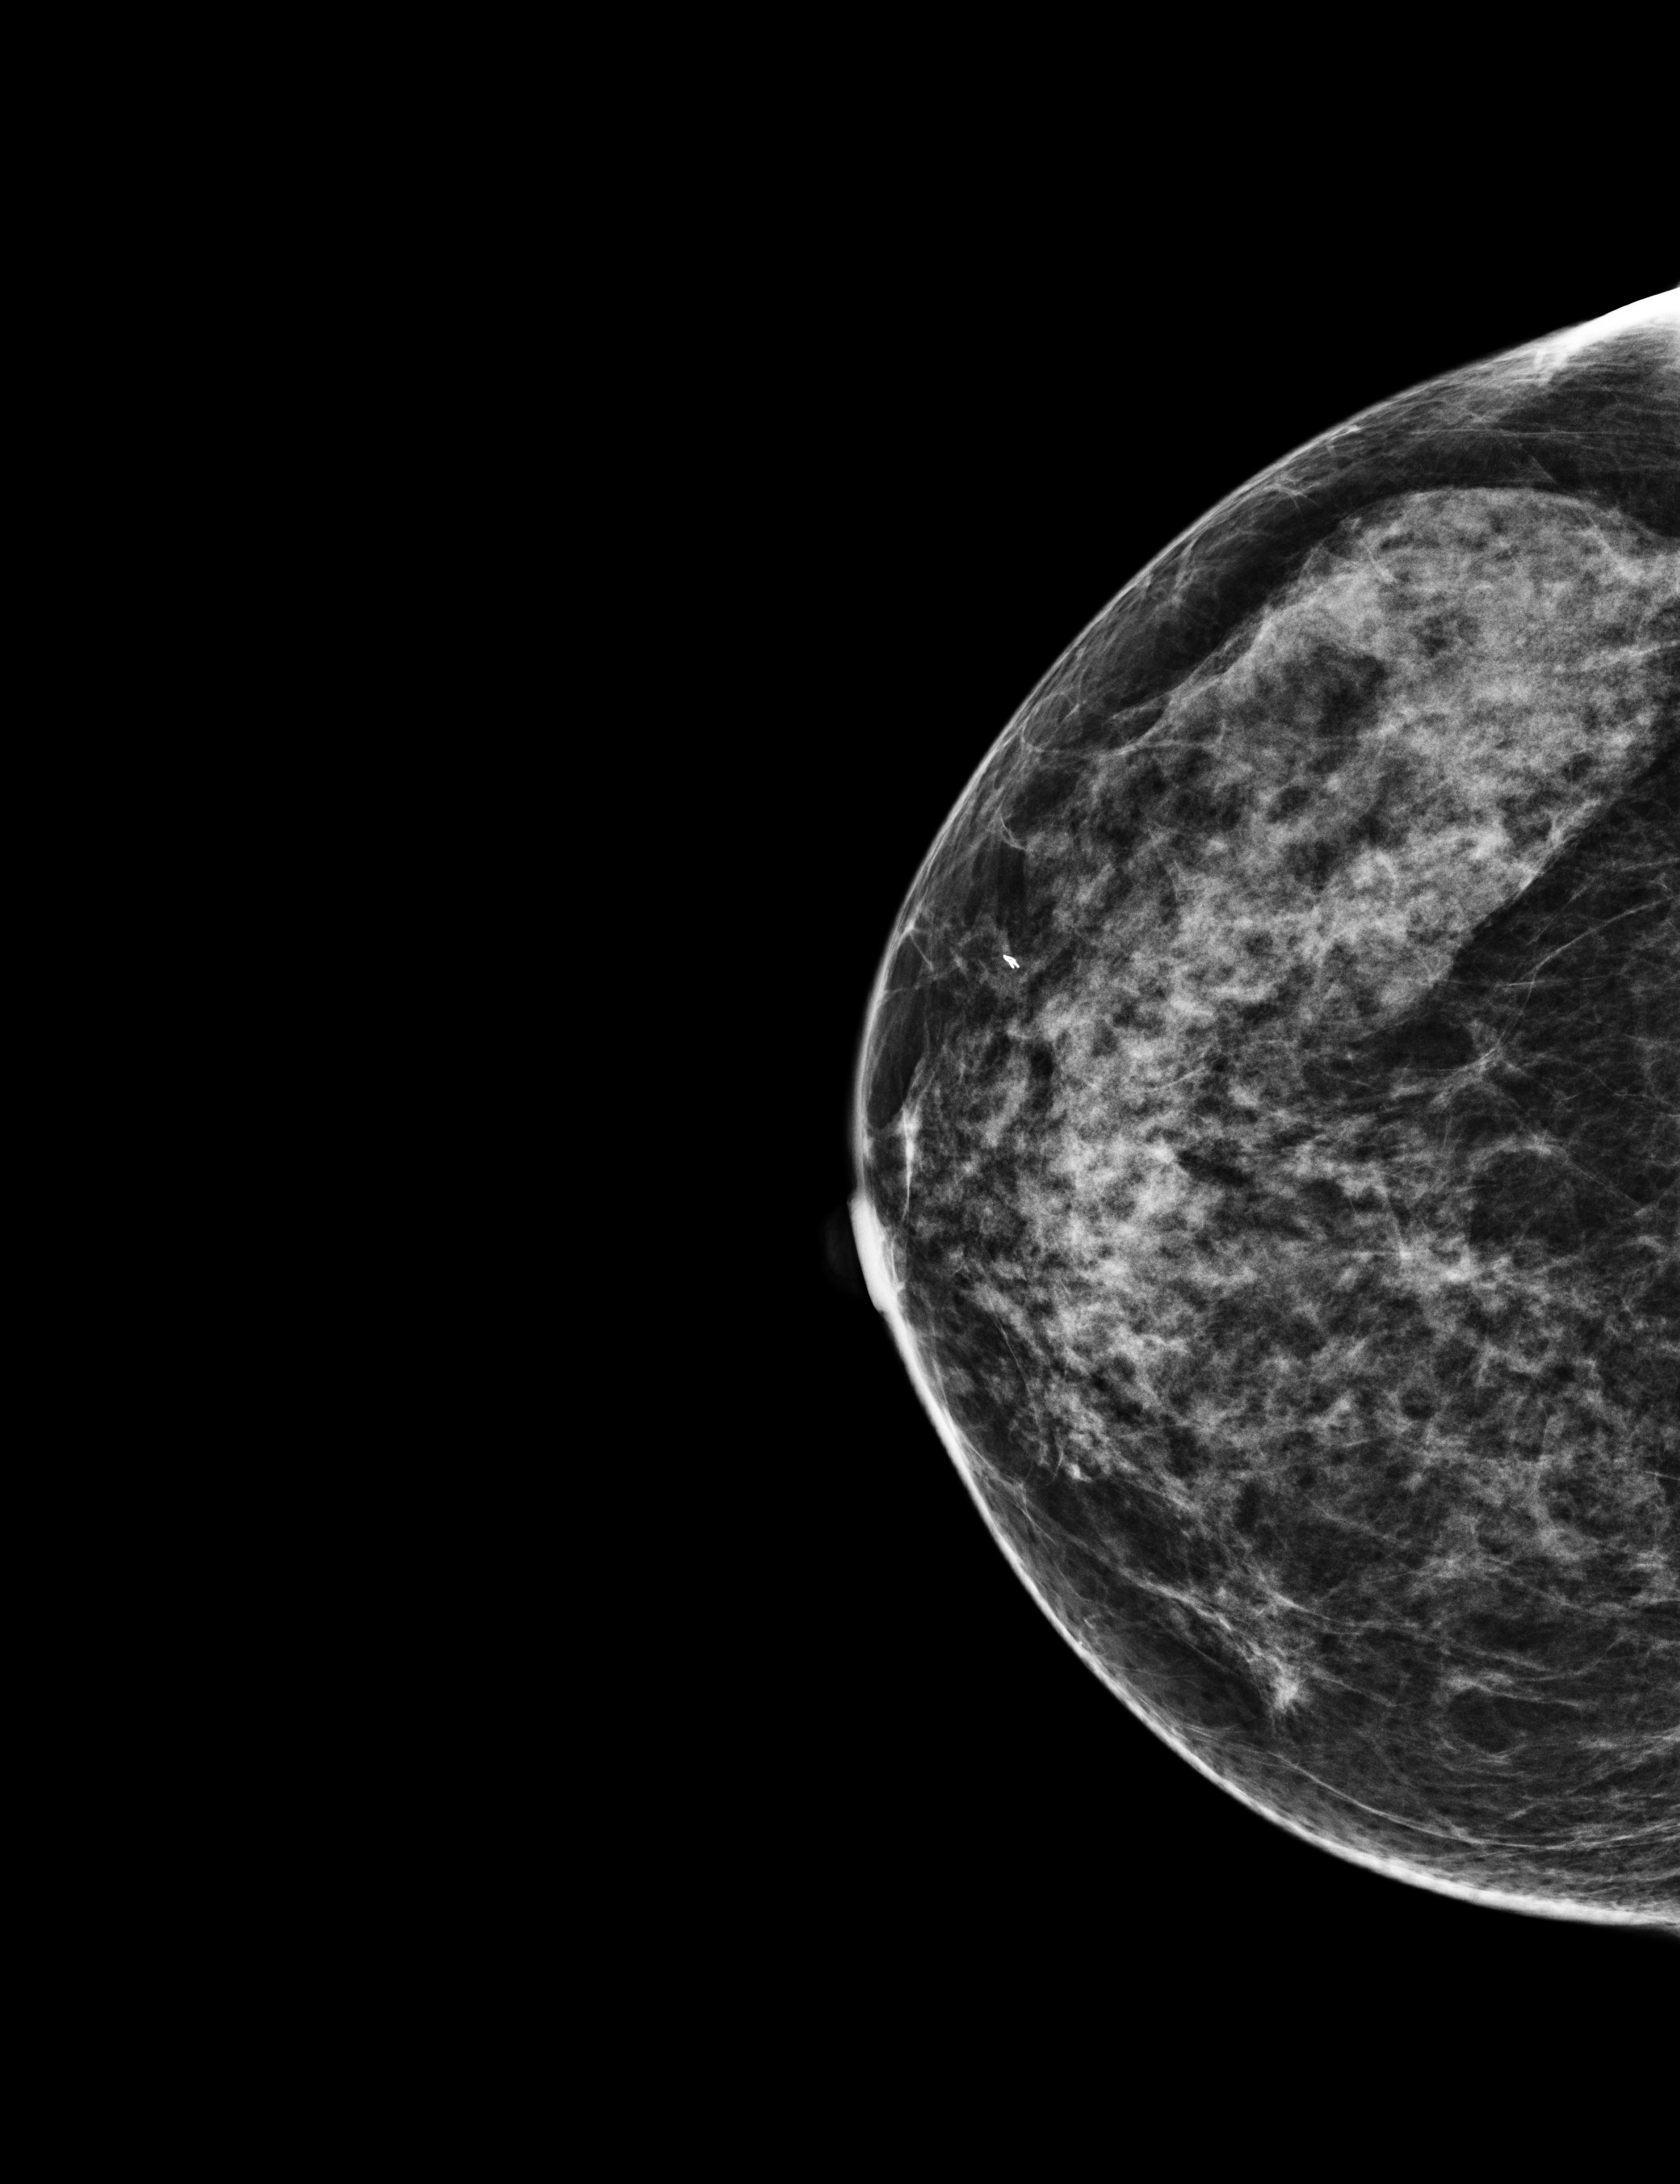
Digital mammogram (FFDM), right breast, cranio-caudal projection, screening examination, system: Selenia Dimensions. Female patient, age 61 years.
Breast density at the screening exam (both breasts): heterogeneously dense (BI-RADS density category c). Final BI-RADS category for the screening round (tomosynthesis exam, both breasts): category 1. Recall: no recall after this screen.